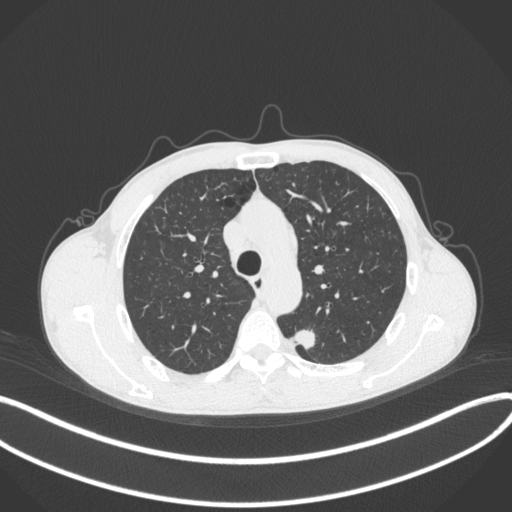
Chest CT, one axial slice; position 285 of 429 along the scan axis; reconstruction kernel B31f; 120 kVp; lung window (W 1500 / L -600 HU); 1 mm slice thickness; 512 × 512 image matrix. Male patient, age 51 years. From the clinical record (not read from this slice): clinical TNM (as recorded): T2a N1 M1.
Annotated regions visible in this slice (bounding box drawn by a radiologist):
- lung tumour (recorded histology: adenocarcinoma): bounding box (x1, y1, x2, y2) in pixels: (289, 324, 323, 355)